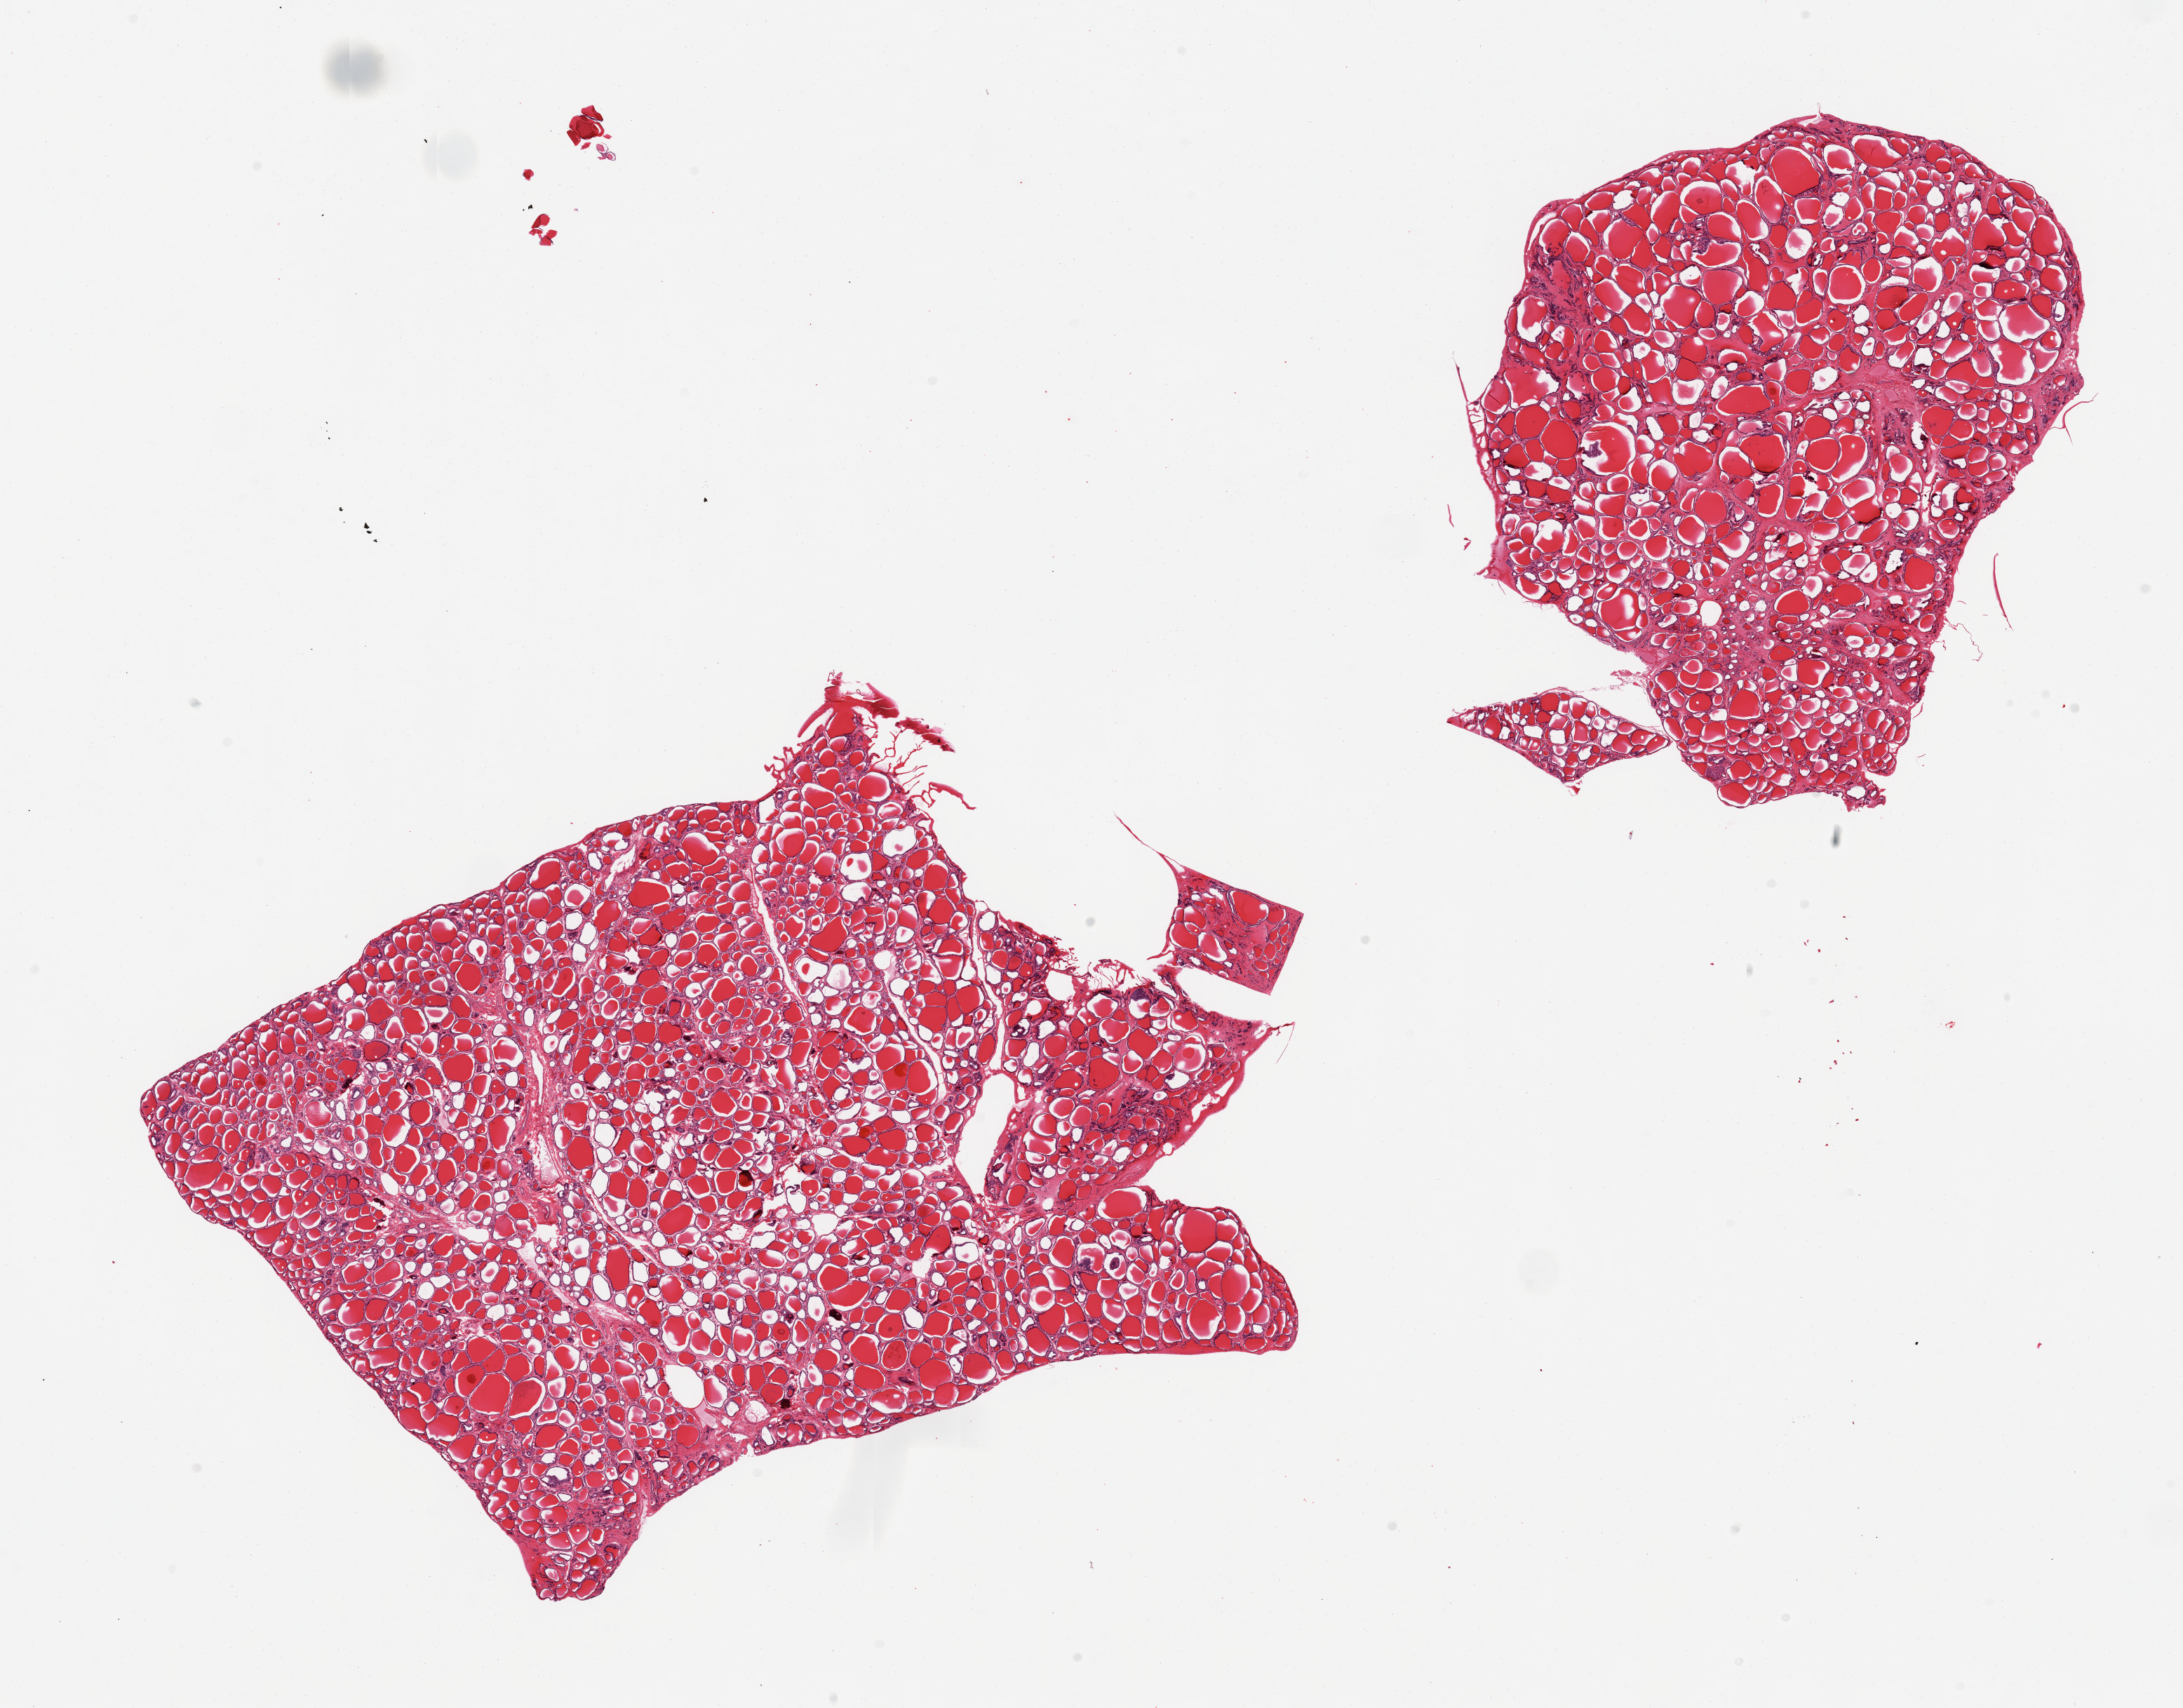
Whole-slide image, hematoxylin and eosin (H&E) stain — shown as a low-resolution overview of the whole scanned area (about 24.6 x 19.3 mm). PAXgene-fixed paraffin-embedded (PFPE) section. Sampled site (target tissue): thyroid. Donor tissue sample. Donor: male.
Review note (as recorded): 2 pieces; well dissected.